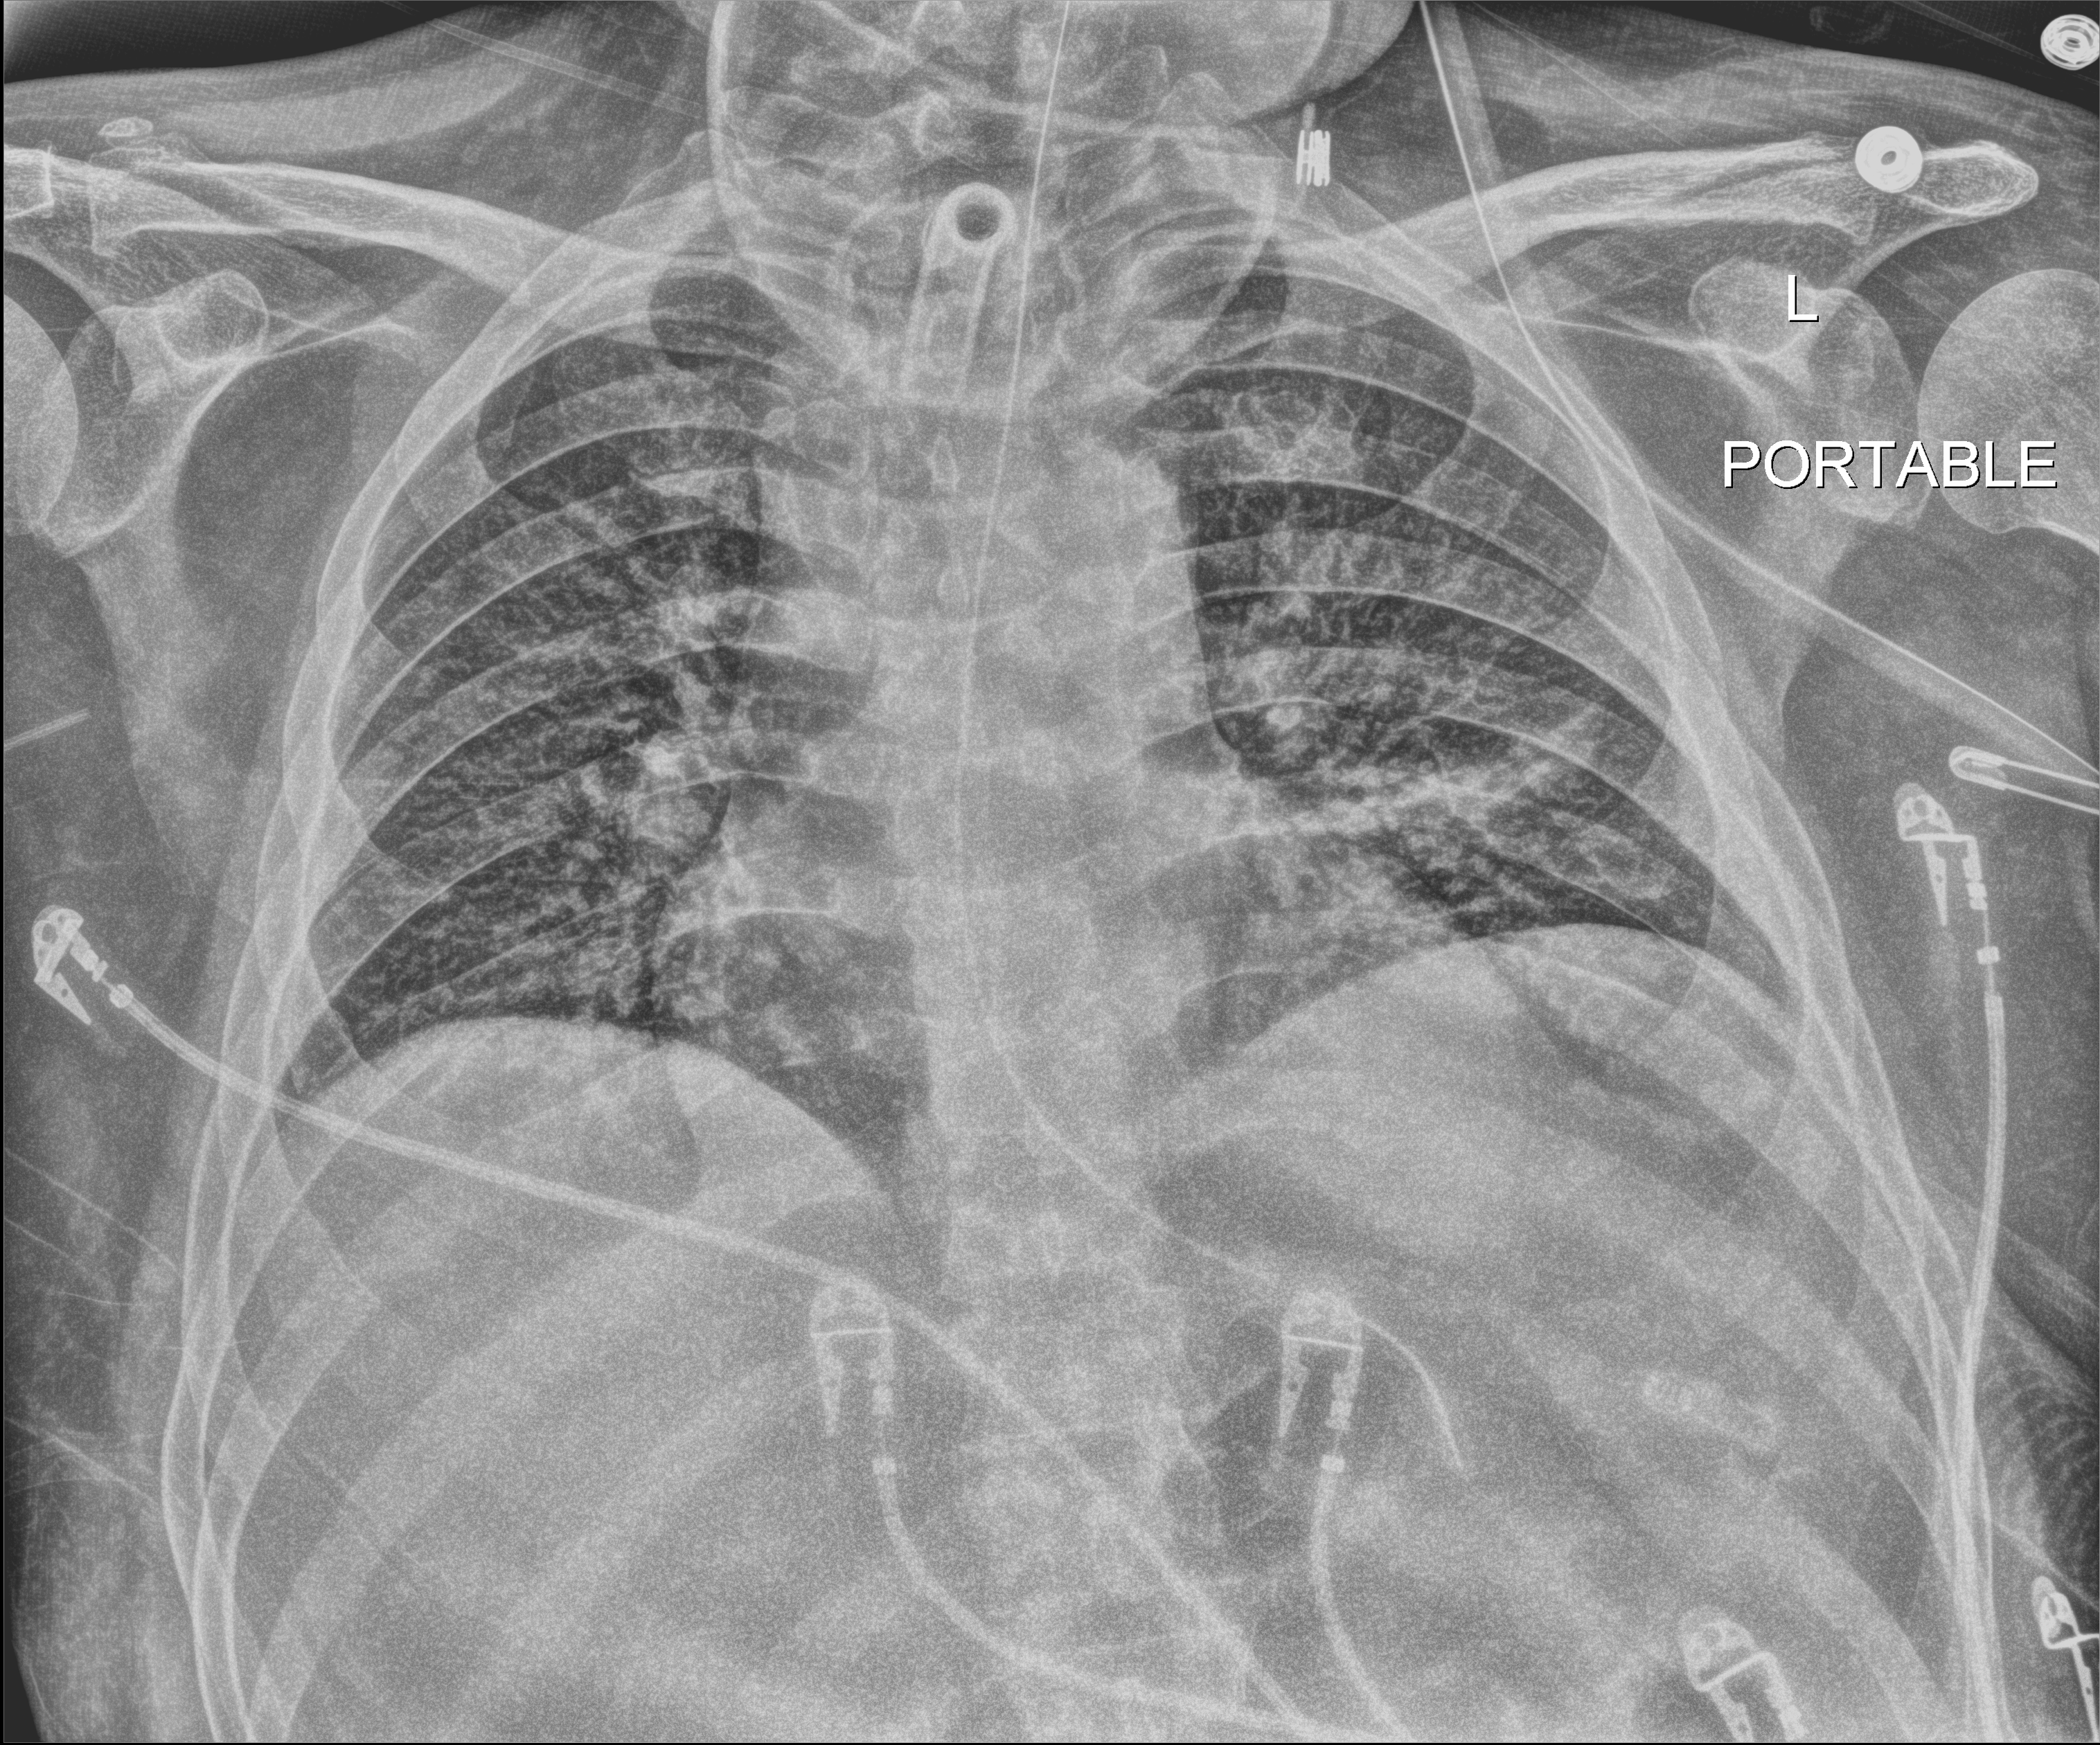
Bedside chest radiograph (digital radiography). Patient hospitalised with COVID-19; male, aged 18–59 years.
Hospital-stay facts (about this admission, not read from this image; timing relative to this image not recorded):
- mechanically ventilated during this hospital stay: yes
- length of hospital stay: 65 days